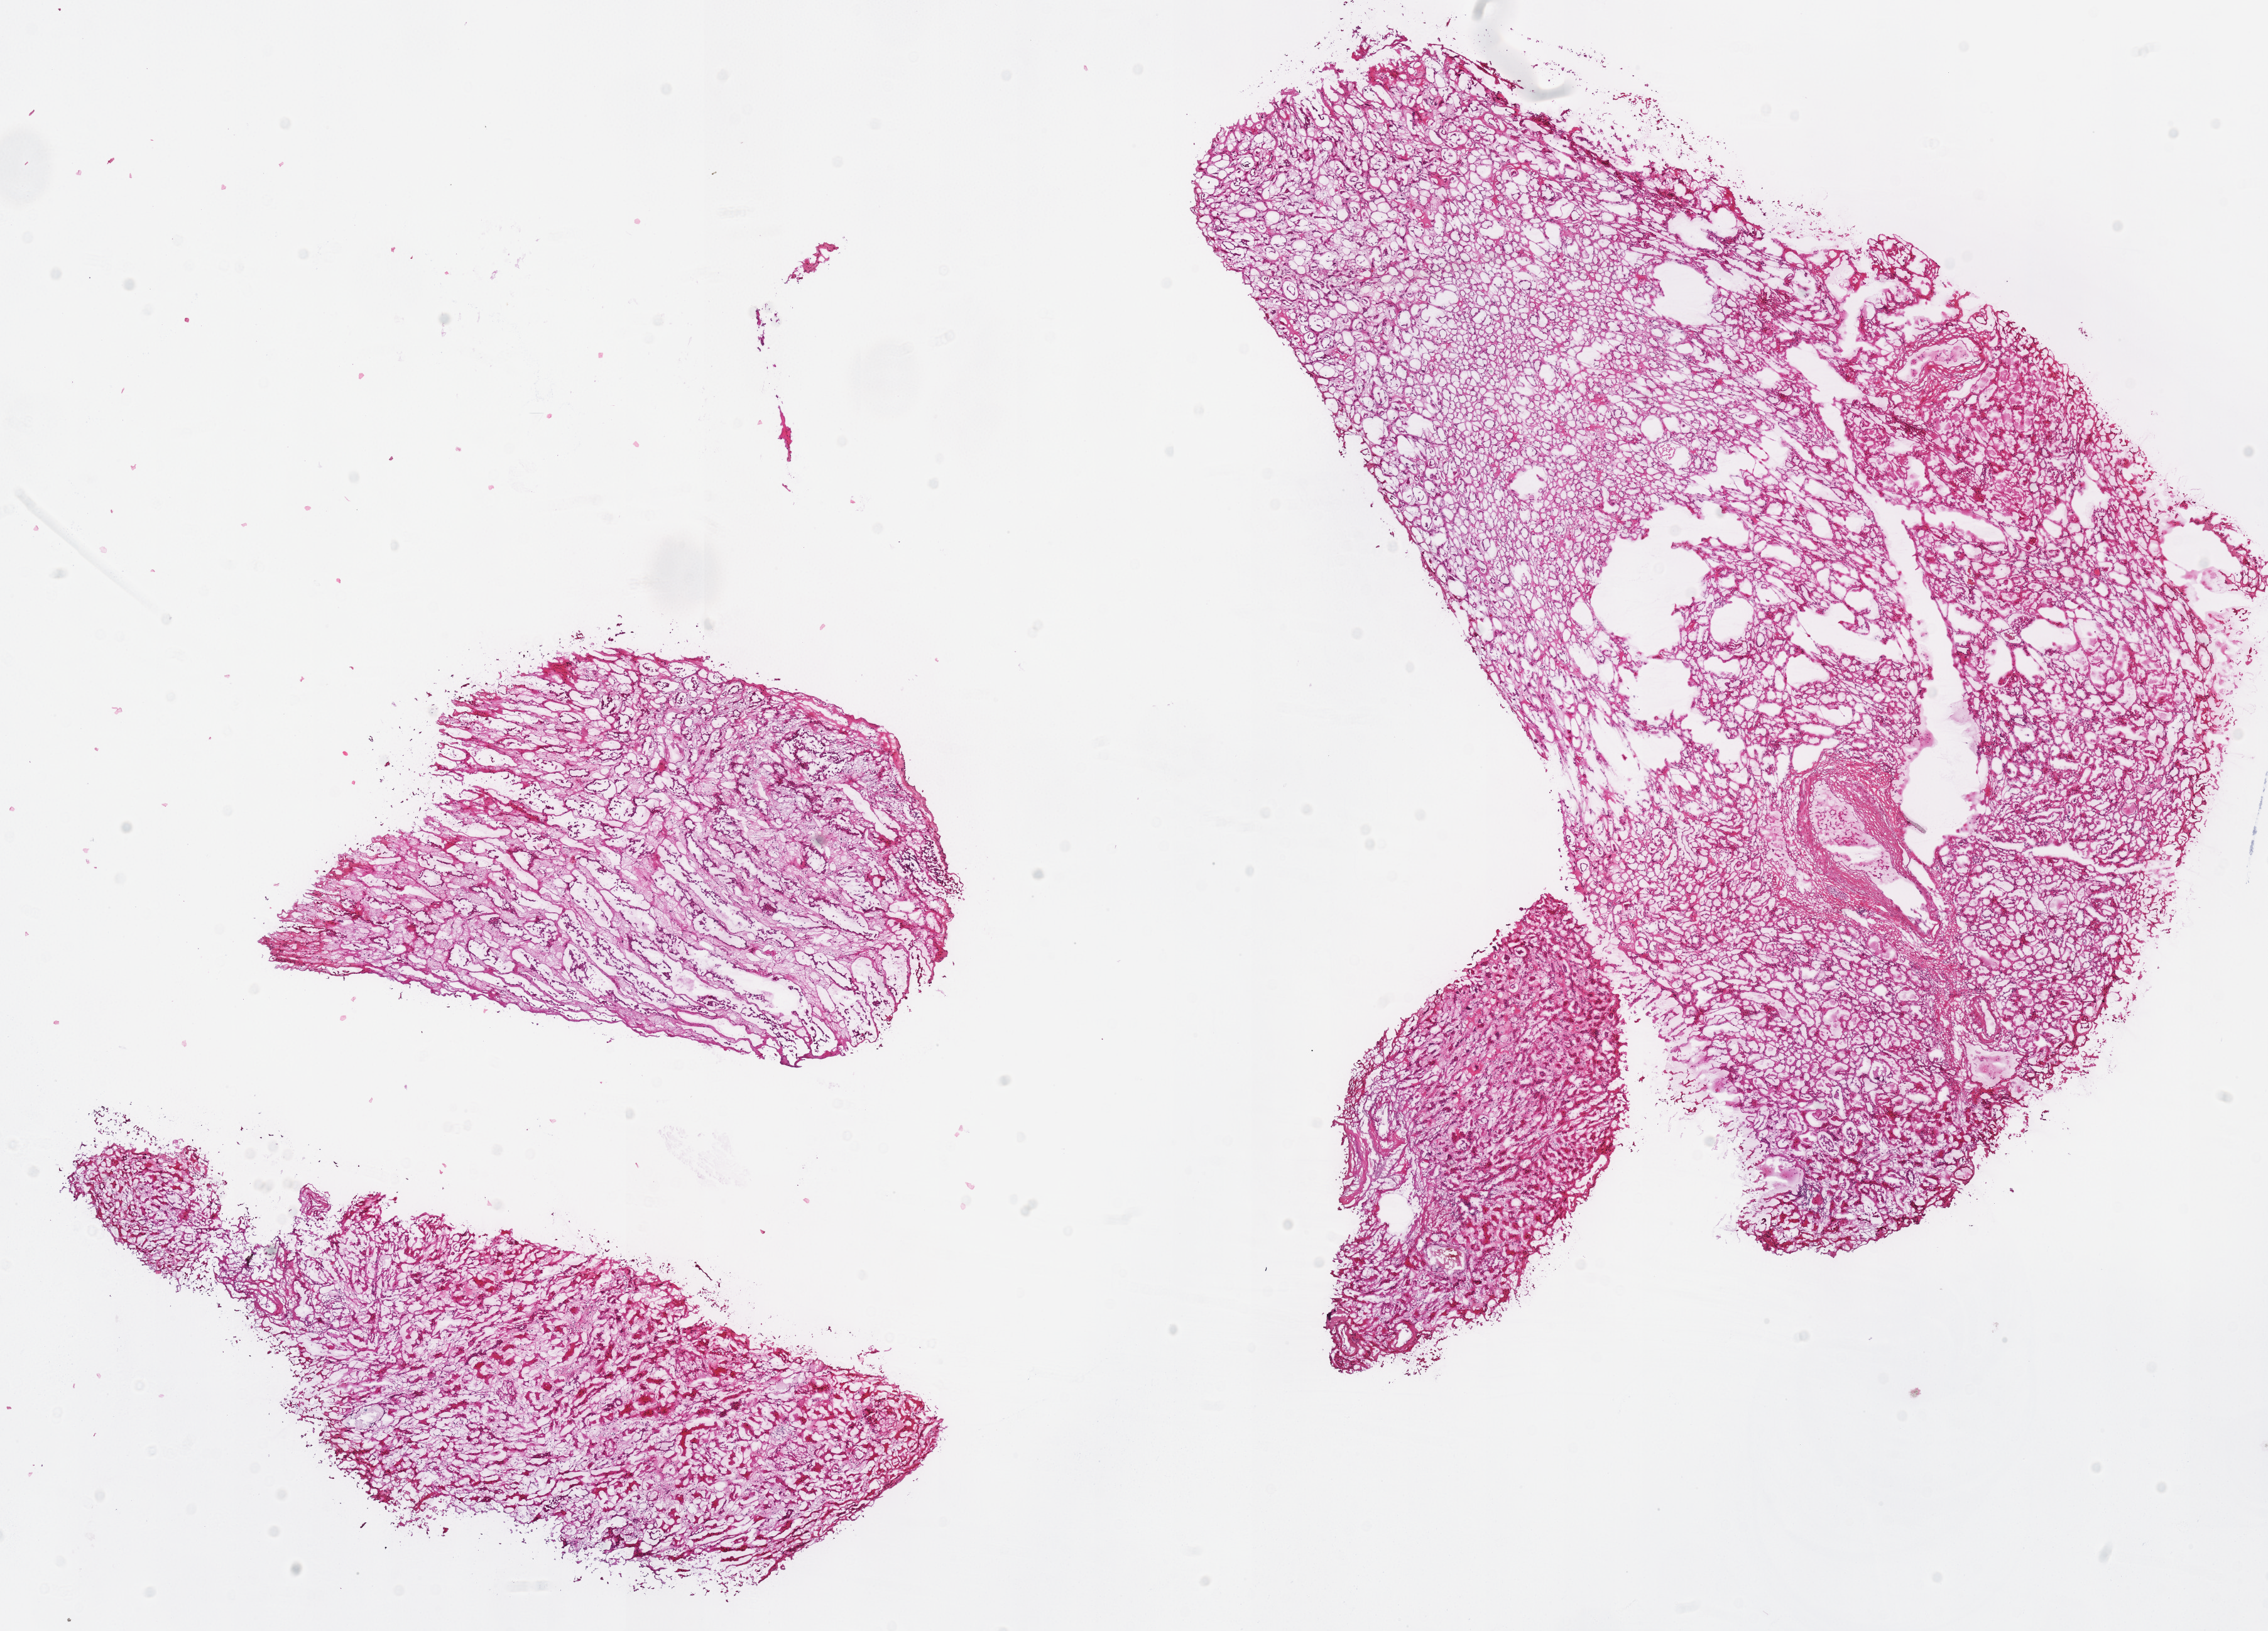
Digitized H&E tissue section (whole slide) — shown as a low-resolution overview of the whole scanned area (about 14.2 x 10.2 mm), frozen section from the top of the tissue portion, solid tissue normal (non-tumour tissue) sample from the kidney. Patient: male, age at initial diagnosis 78 years.
This section: solid tissue normal sample (biorepository sample class). Patient diagnosis: Renal cell carcinoma, chromophobe type.